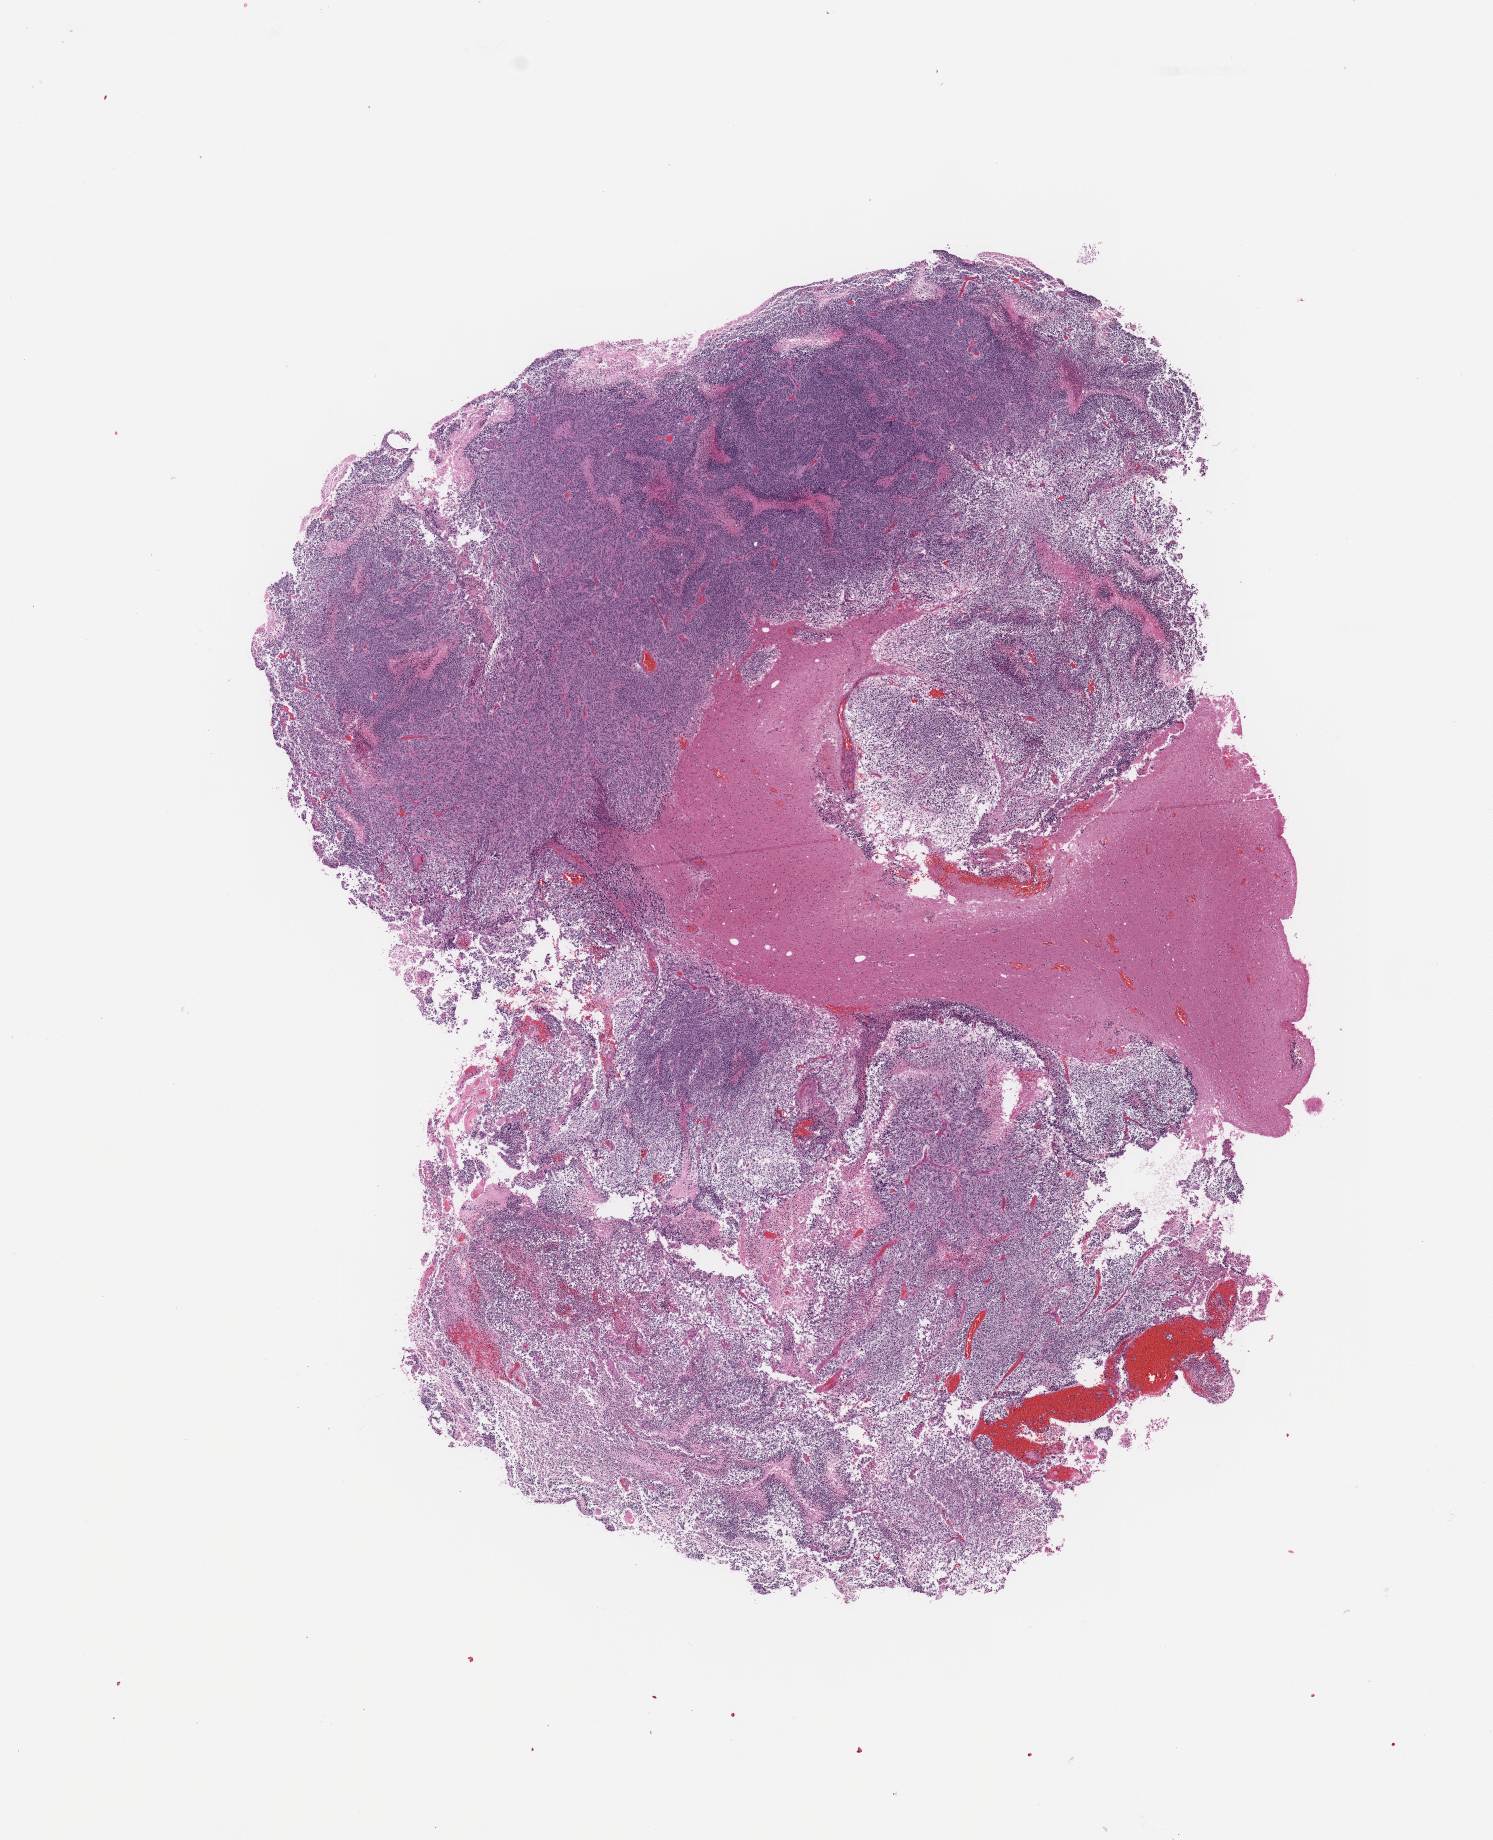
Whole-slide histology image, Hematoxylin and eosin (H&E) stained — whole scanned area (about 11.8 x 14.6 mm, acquisition: 20x scan) shown as a low-resolution overview; tumour tissue sample, sampled site: brain. 48-year-old male patient.
Diagnosis: Glioblastoma.